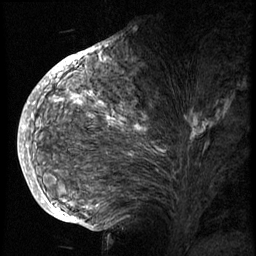
Breast MRI (dynamic contrast-enhanced), one sagittal slice; position 39 of 74 along the scan axis; 3 images stored at this slice position (order not interpretable as contrast timing); 1.5 T; TE 4.2 ms, TR 8.9 ms; 2.5 mm slice thickness; 256 × 256 image matrix, field of view 200 × 200 mm. Patient: female, 57 years. From the clinical record (not read from this slice): setting: breast cancer imaged before/during neoadjuvant chemotherapy; receptor status: HER2-positive.
Structures marked on this image (semi-automatically segmented with operator editing):
- analysis volume of interest (the breast-tissue region the enhancement analysis was run in; not a lesion): bounding box <40,62,241,175> (left, top, right, bottom; pixels)
- tumour enhancement mask (voxels above the 140 % enhancement threshold inside the analysis volume of interest): <54,62,147,132>